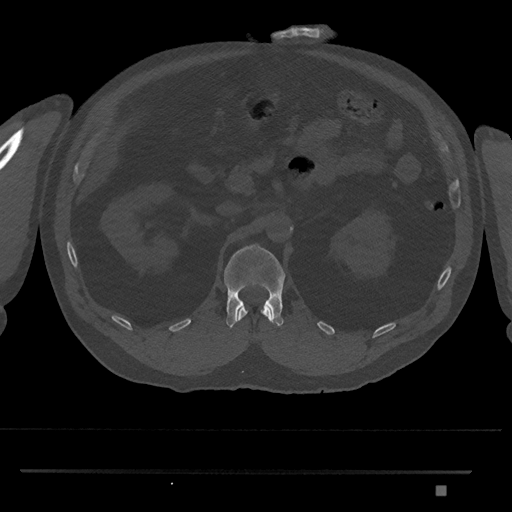
CT including the spine, one axial slice; reconstruction kernel Br40s/3; 120 kVp; bone window (W 1800 / L 400 HU); 0.5 mm slice thickness; 512 × 512 image matrix. Patient: male, 65 years. Case-level facts recorded for this patient, not image findings: primary cancer: prostate.
Outlined on this slice (semi-automatic segmentation, software-assisted and operator-edited):
- L1 vertebra: bounding box [x1, y1, x2, y2] px = [224, 244, 285, 328]
- T12 vertebra: [237, 306, 272, 322]